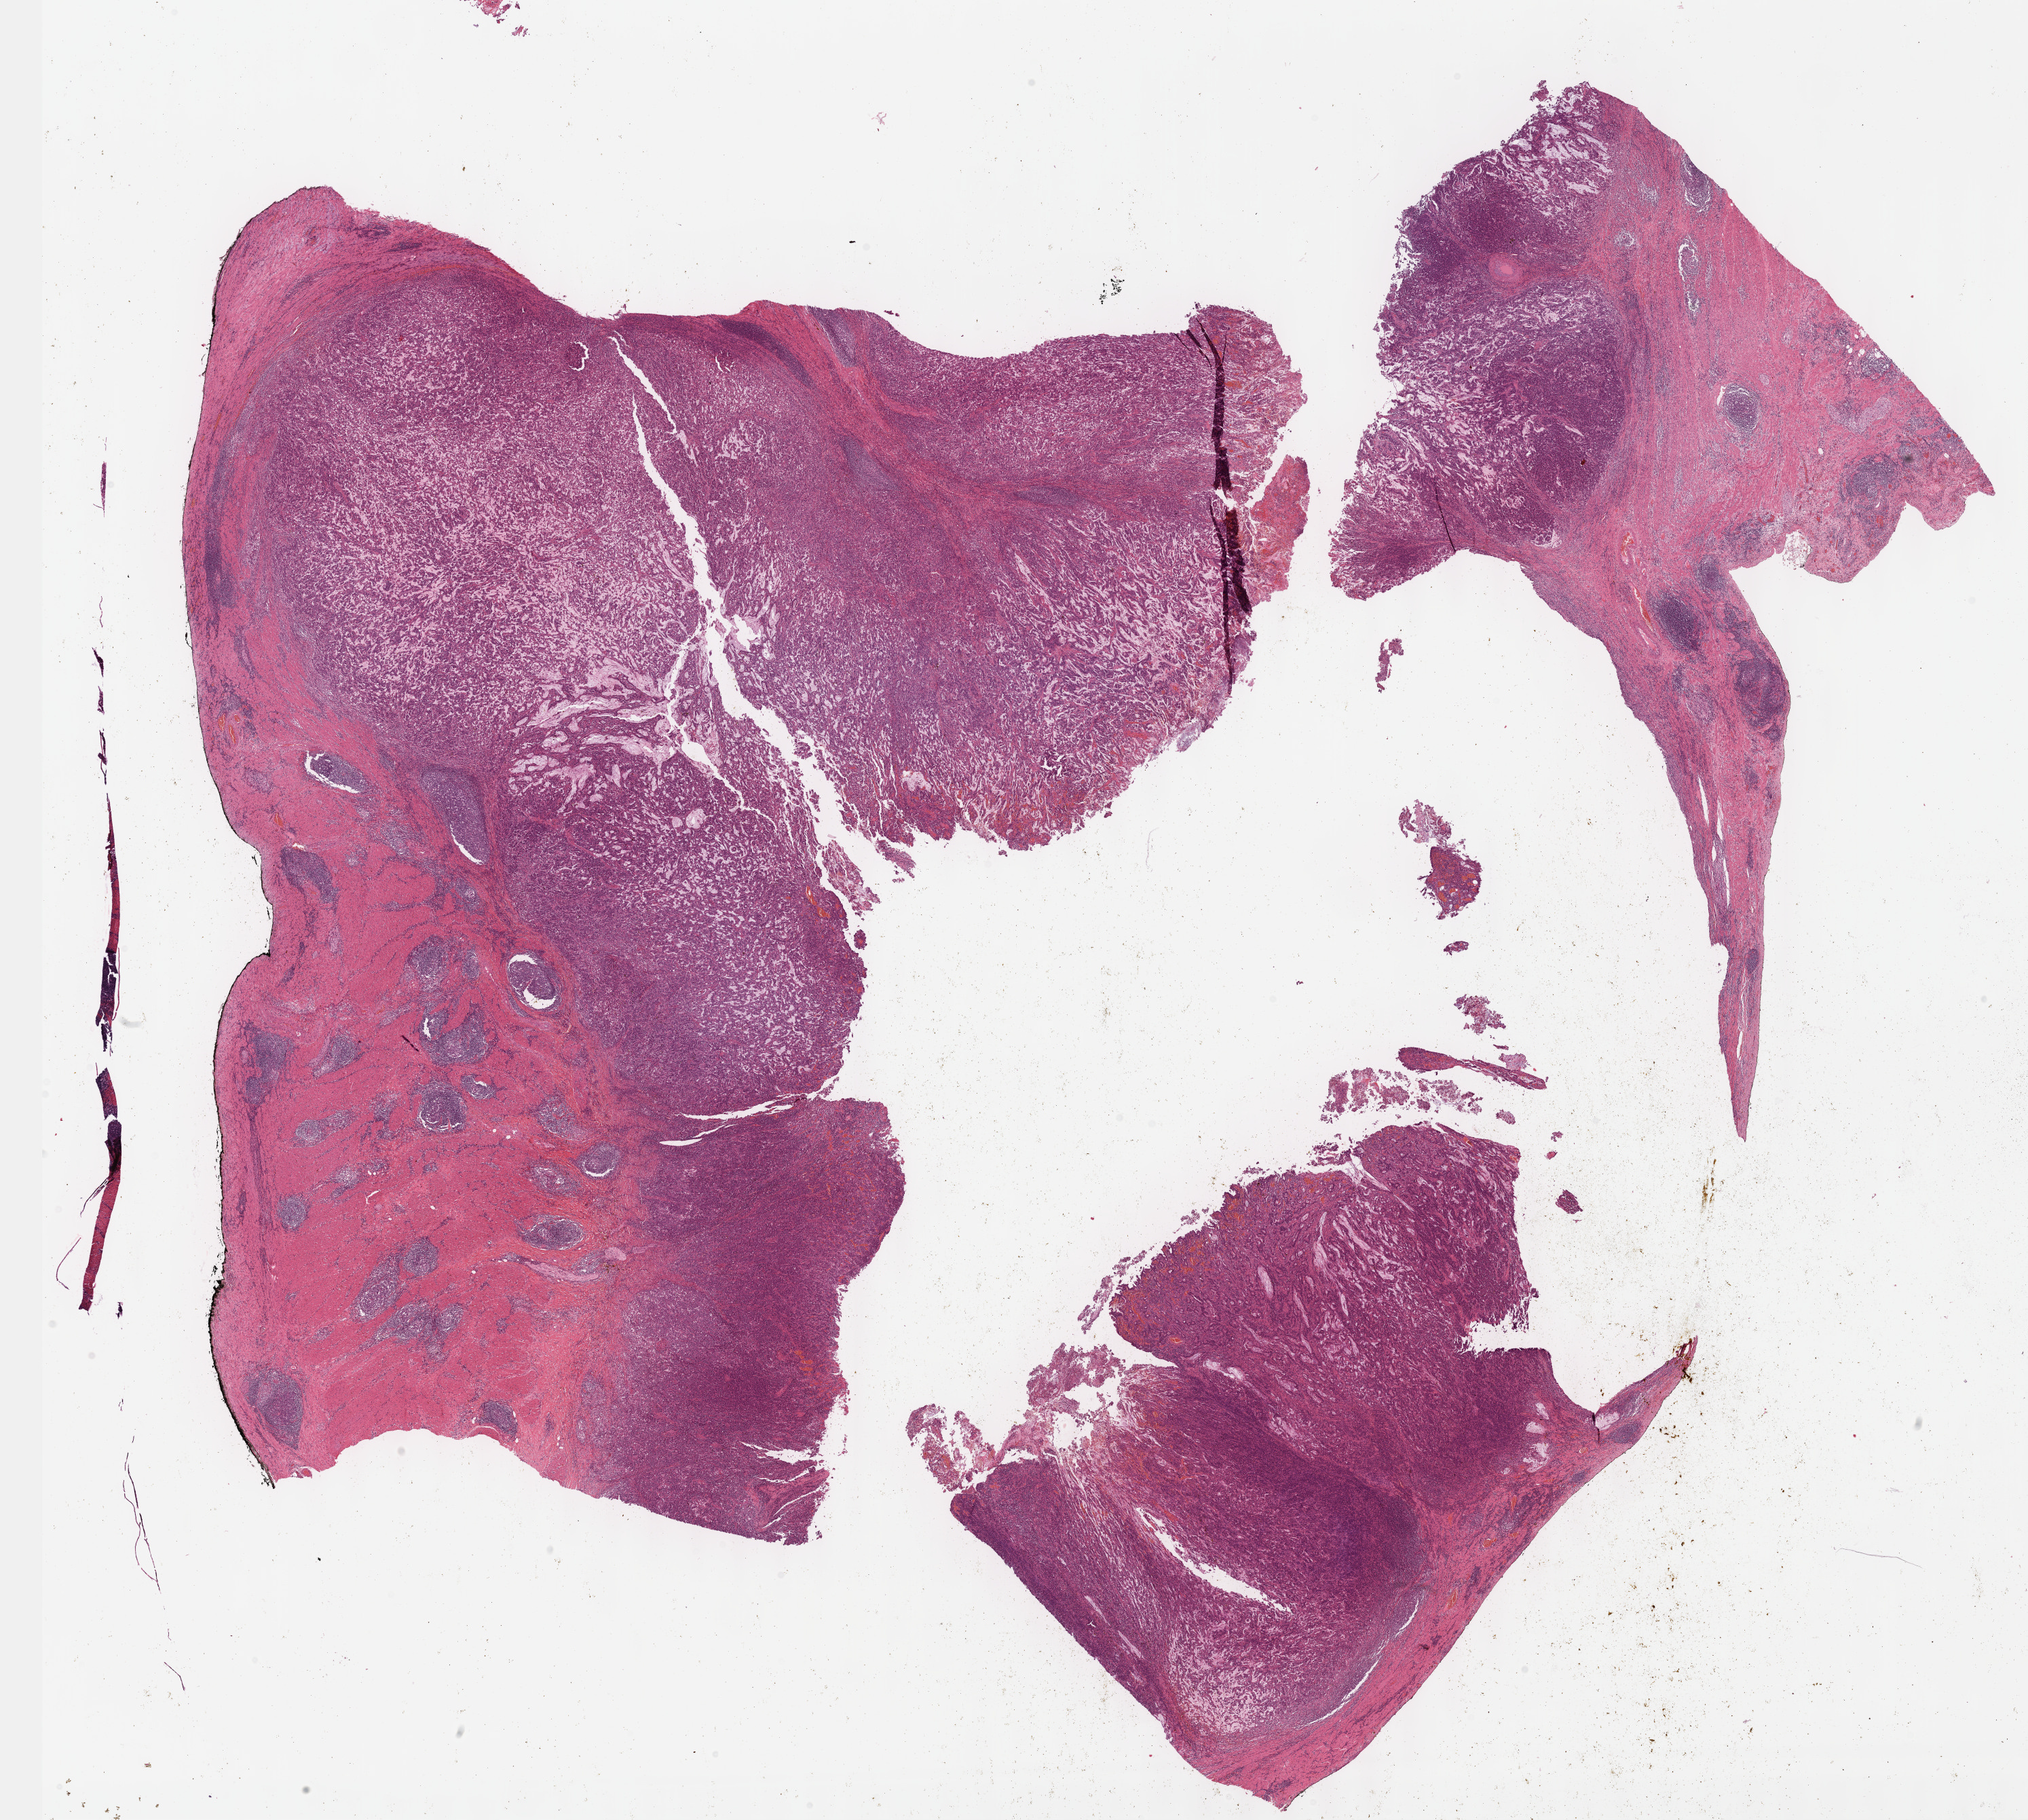
Digitized Hematoxylin and eosin (H&E) stained tissue section (whole slide) — whole scanned area (about 24.1 x 21.7 mm, from a 40x scan) shown as a low-resolution overview; formalin-fixed paraffin-embedded (FFPE) diagnostic section; primary tumour sample from the stomach. Patient: male, age at initial diagnosis 74 years. Histologic grade: G3 (poorly differentiated).
AJCC pathologic stage: IIB (7th edition). Lymph nodes positive (case pathology): 0 of 26 examined. Histologic diagnosis: Signet ring cell carcinoma (gastric antrum).